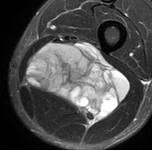
MRI of an extremity soft-tissue mass, one axial slice. Slice 42 of 90 in the series (ordered by position). STIR. MR volume resampled by the dataset authors to the PET/CT grid (not the native acquisition matrix). 3.27 mm slice thickness. 152 × 150 image matrix, field of view 148 × 146 mm. Male patient. Case-level facts recorded for this patient, not image findings: histological type: undifferentiated pleomorphic liposarcoma; grade: high; site of the primary tumour: left thigh.
Outlined on this slice (expert contour drawn on MRI and transferred to this co-registered scan by the dataset authors):
- gross tumour volume including surrounding oedema: bounding box (x1, y1, x2, y2) in pixels: (27, 41, 129, 124)
- gross tumour volume (mass): (27, 43, 129, 124)